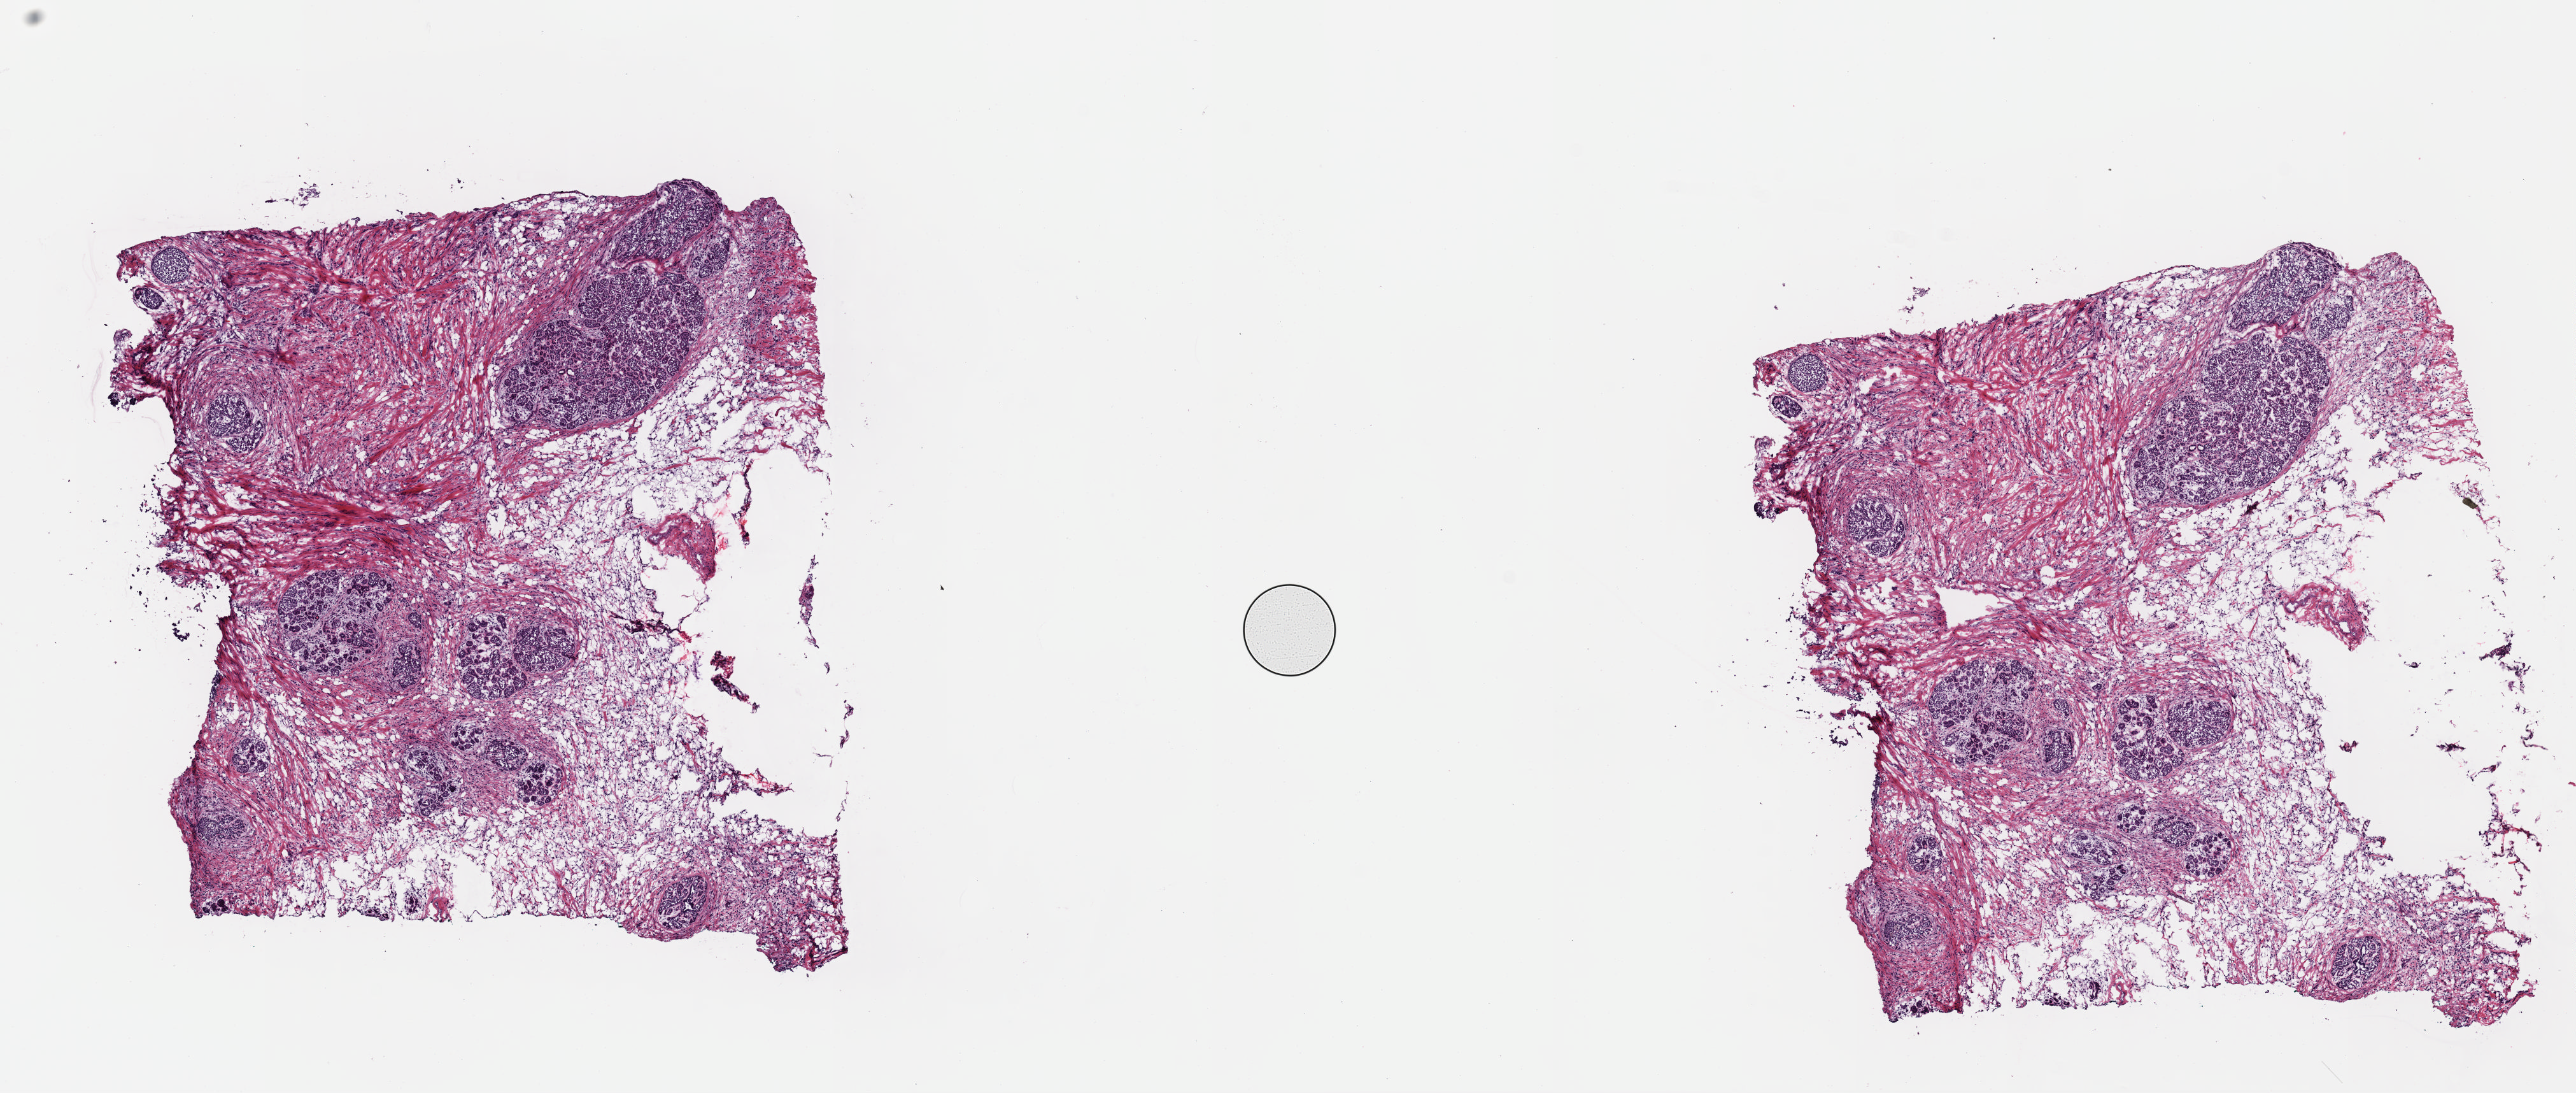
Hematoxylin and eosin (H&E) stained whole-slide image — a low-resolution overview of the entire scanned area, about 16.0 x 6.8 mm. Frozen section from the top of the tissue portion. Primary tumour sample from the breast. Female, age 45 years at initial diagnosis. Slide review estimates, as recorded: tumour cells 60%, tumour nuclei 65%.
Histologic diagnosis: Lobular carcinoma, NOS.